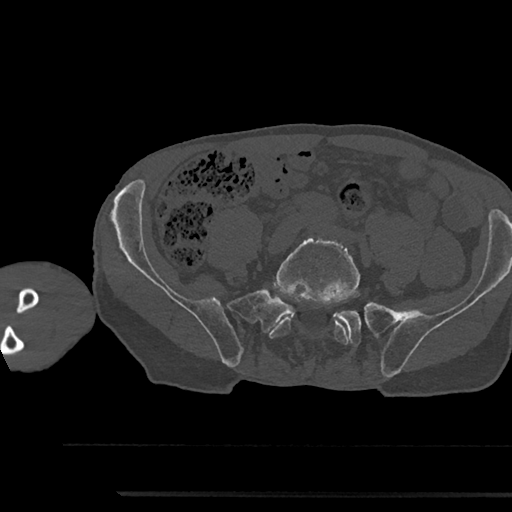
CT including the spine, one axial slice. Slice 323 of 797 in the series (ordered by position). Reconstruction kernel Br40s/3. 120 kVp. Bone window (W 1800 / L 400 HU). 0.5 mm slice thickness. 512 × 512 image matrix, field of view 367 × 367 mm. Male patient, age 79 years. Case-level facts recorded for this patient, not image findings: primary cancer: prostate.
Outlined on this slice (semi-automatic segmentation, software-assisted and operator-edited):
- L5 vertebra: bounding box (x1, y1, x2, y2) in pixels: (269, 235, 360, 345)